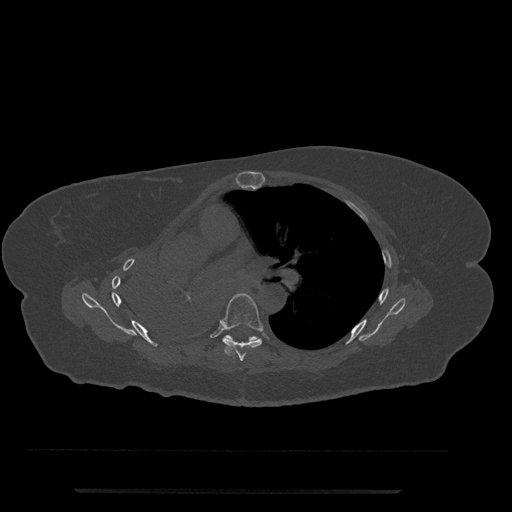
CT including the spine, one axial slice; reconstruction kernel Br40s/3; bone window (W 1800 / L 400 HU); 512 × 512 image matrix. Female patient, age 51 years. Case-level facts recorded for this patient, not image findings: primary cancer: neuro.
Structures marked on this image (semi-automatic segmentation, software-assisted and operator-edited):
- T6 vertebra: bounding box [x1, y1, x2, y2] px = [221, 293, 263, 361]
- T7 vertebra: [226, 335, 259, 341]